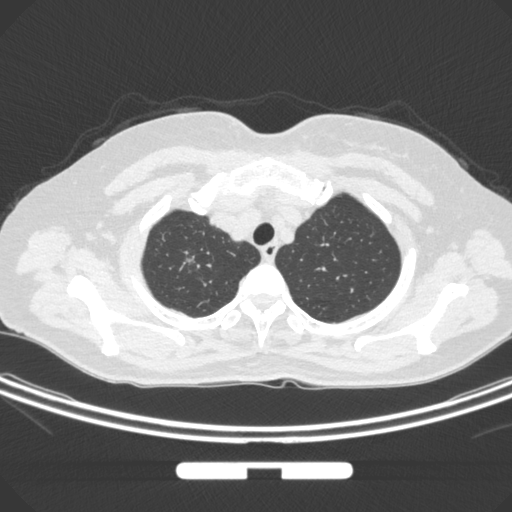
Chest CT, one axial slice; position 253 of 295 along the scan axis; 120 kVp; lung window (W 1500 / L -600 HU); 1 mm slice thickness; 512 × 512 image matrix. Female patient, age 58 years. From the clinical record (not read from this slice): clinical TNM (as recorded): T1b N0 M0; histopathological grade: G2-3.
Annotated regions visible in this slice (bounding box drawn by a radiologist):
- lung tumour (recorded histology: adenocarcinoma): bounding box <175,244,201,274> (left, top, right, bottom; pixels)